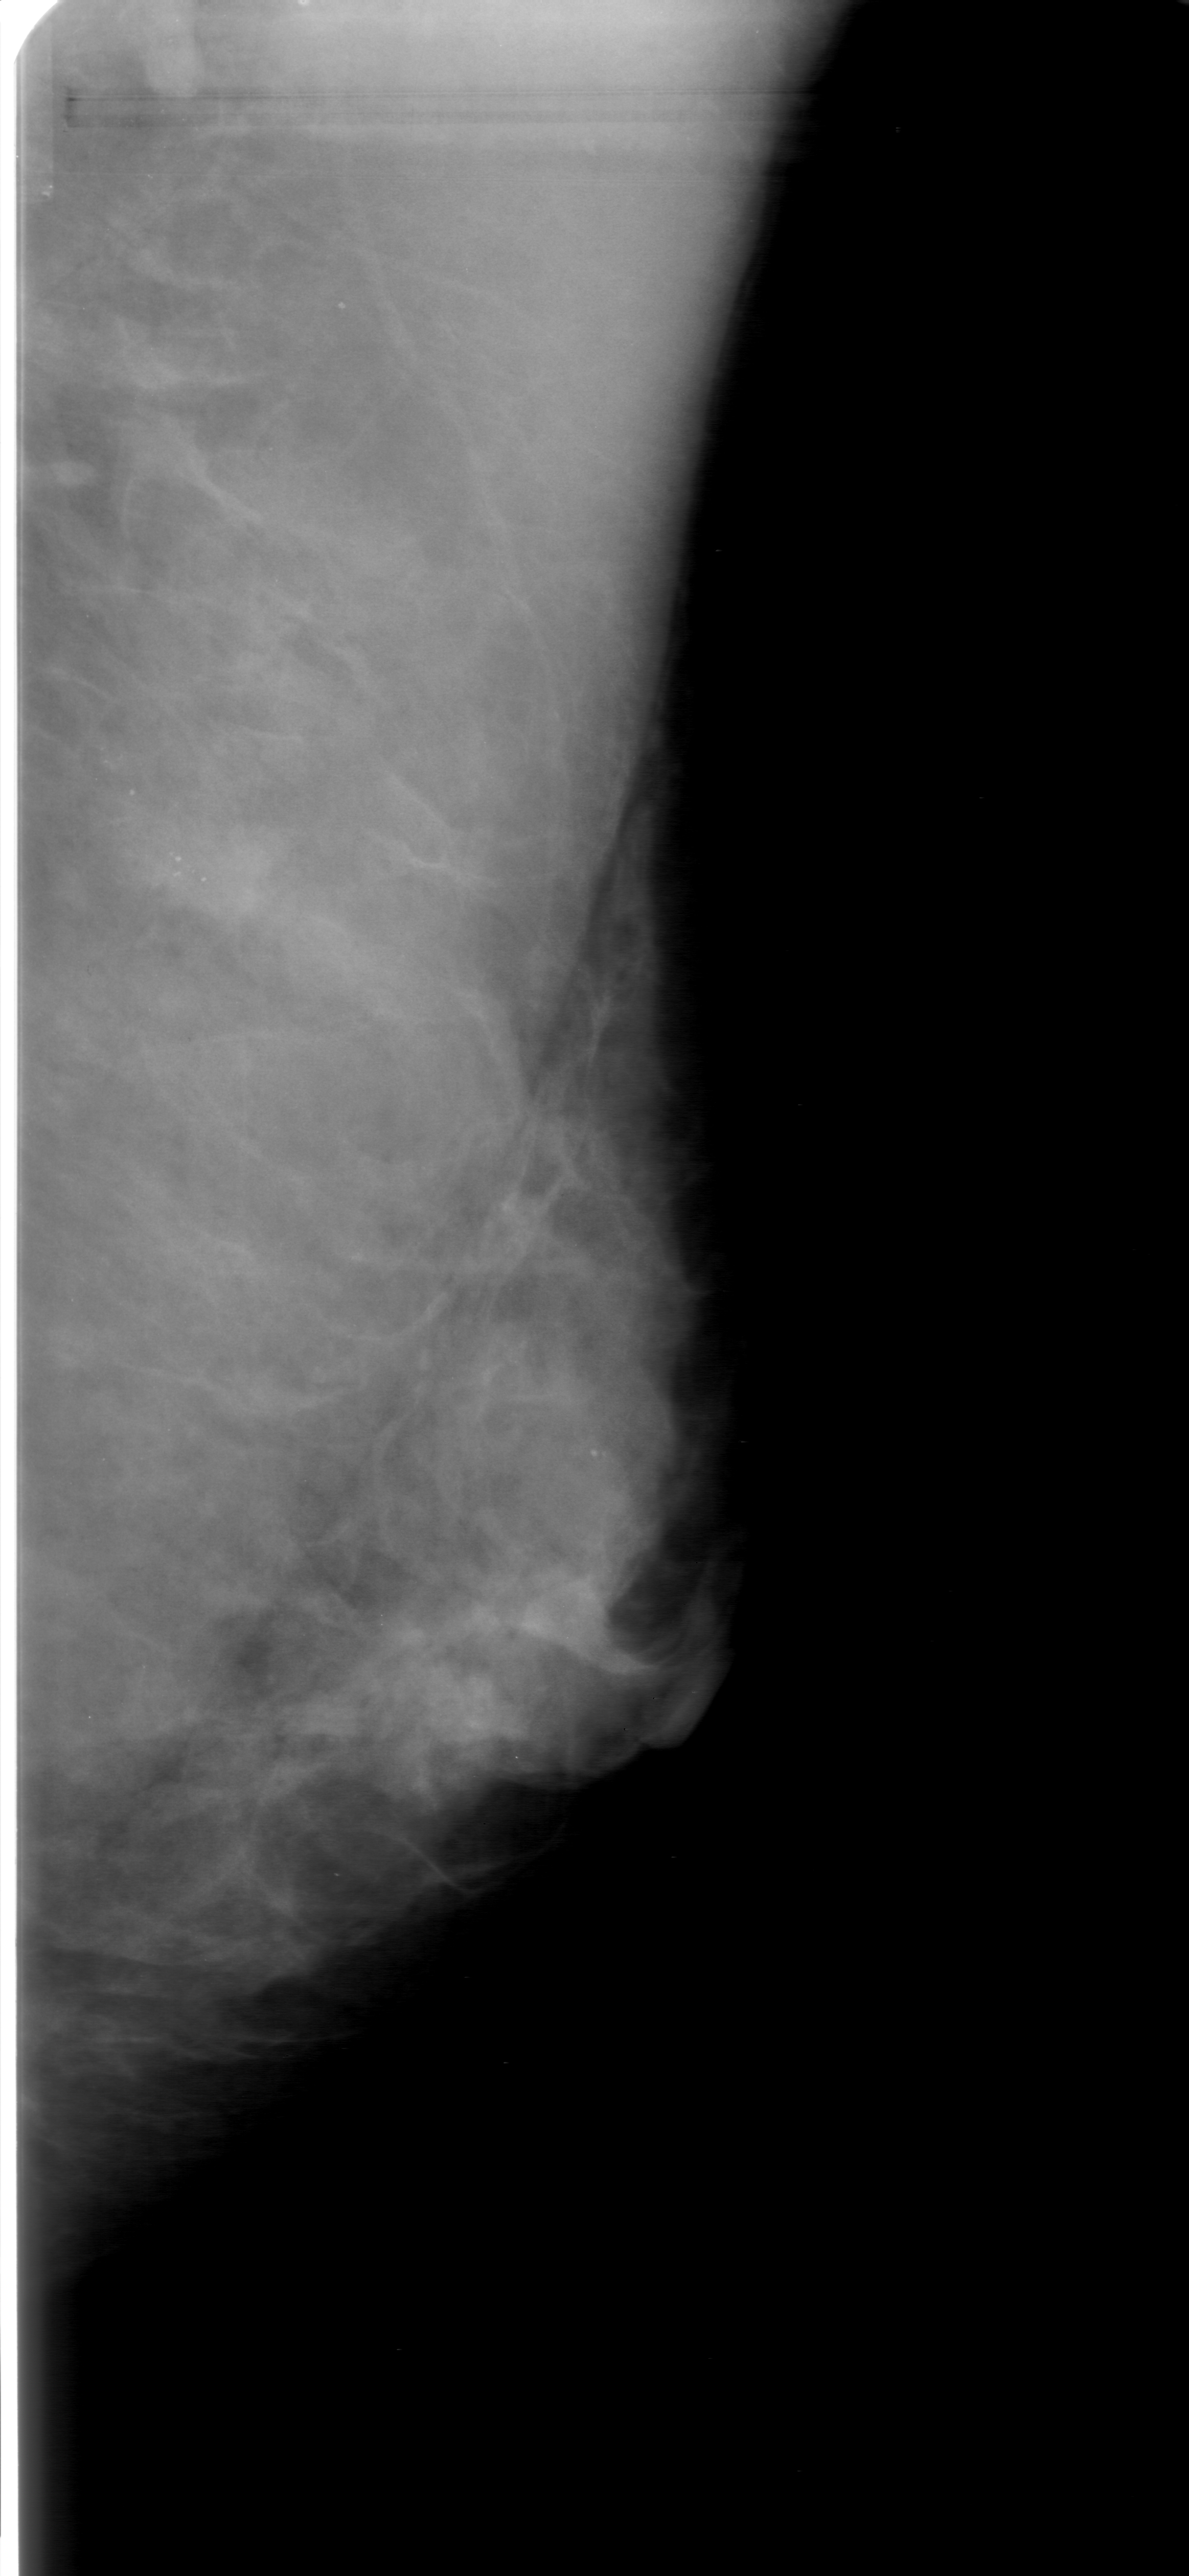
Scanned film-screen mammogram; left breast; mediolateral oblique (MLO) view; BI-RADS breast density category 3 (scale 1–4); 1189 × 2576 image matrix.
Expert-marked regions of interest on this film, with their recorded descriptors:
- calcifications, morphology round and regular / pleomorphic, distribution clustered; BI-RADS assessment category 0 (incomplete: needs additional imaging); subtlety rating 3 on a 1 (subtle) to 5 (obvious) scale; pathology (as recorded): benign: box from (x=21, y=687) to (x=286, y=961) px